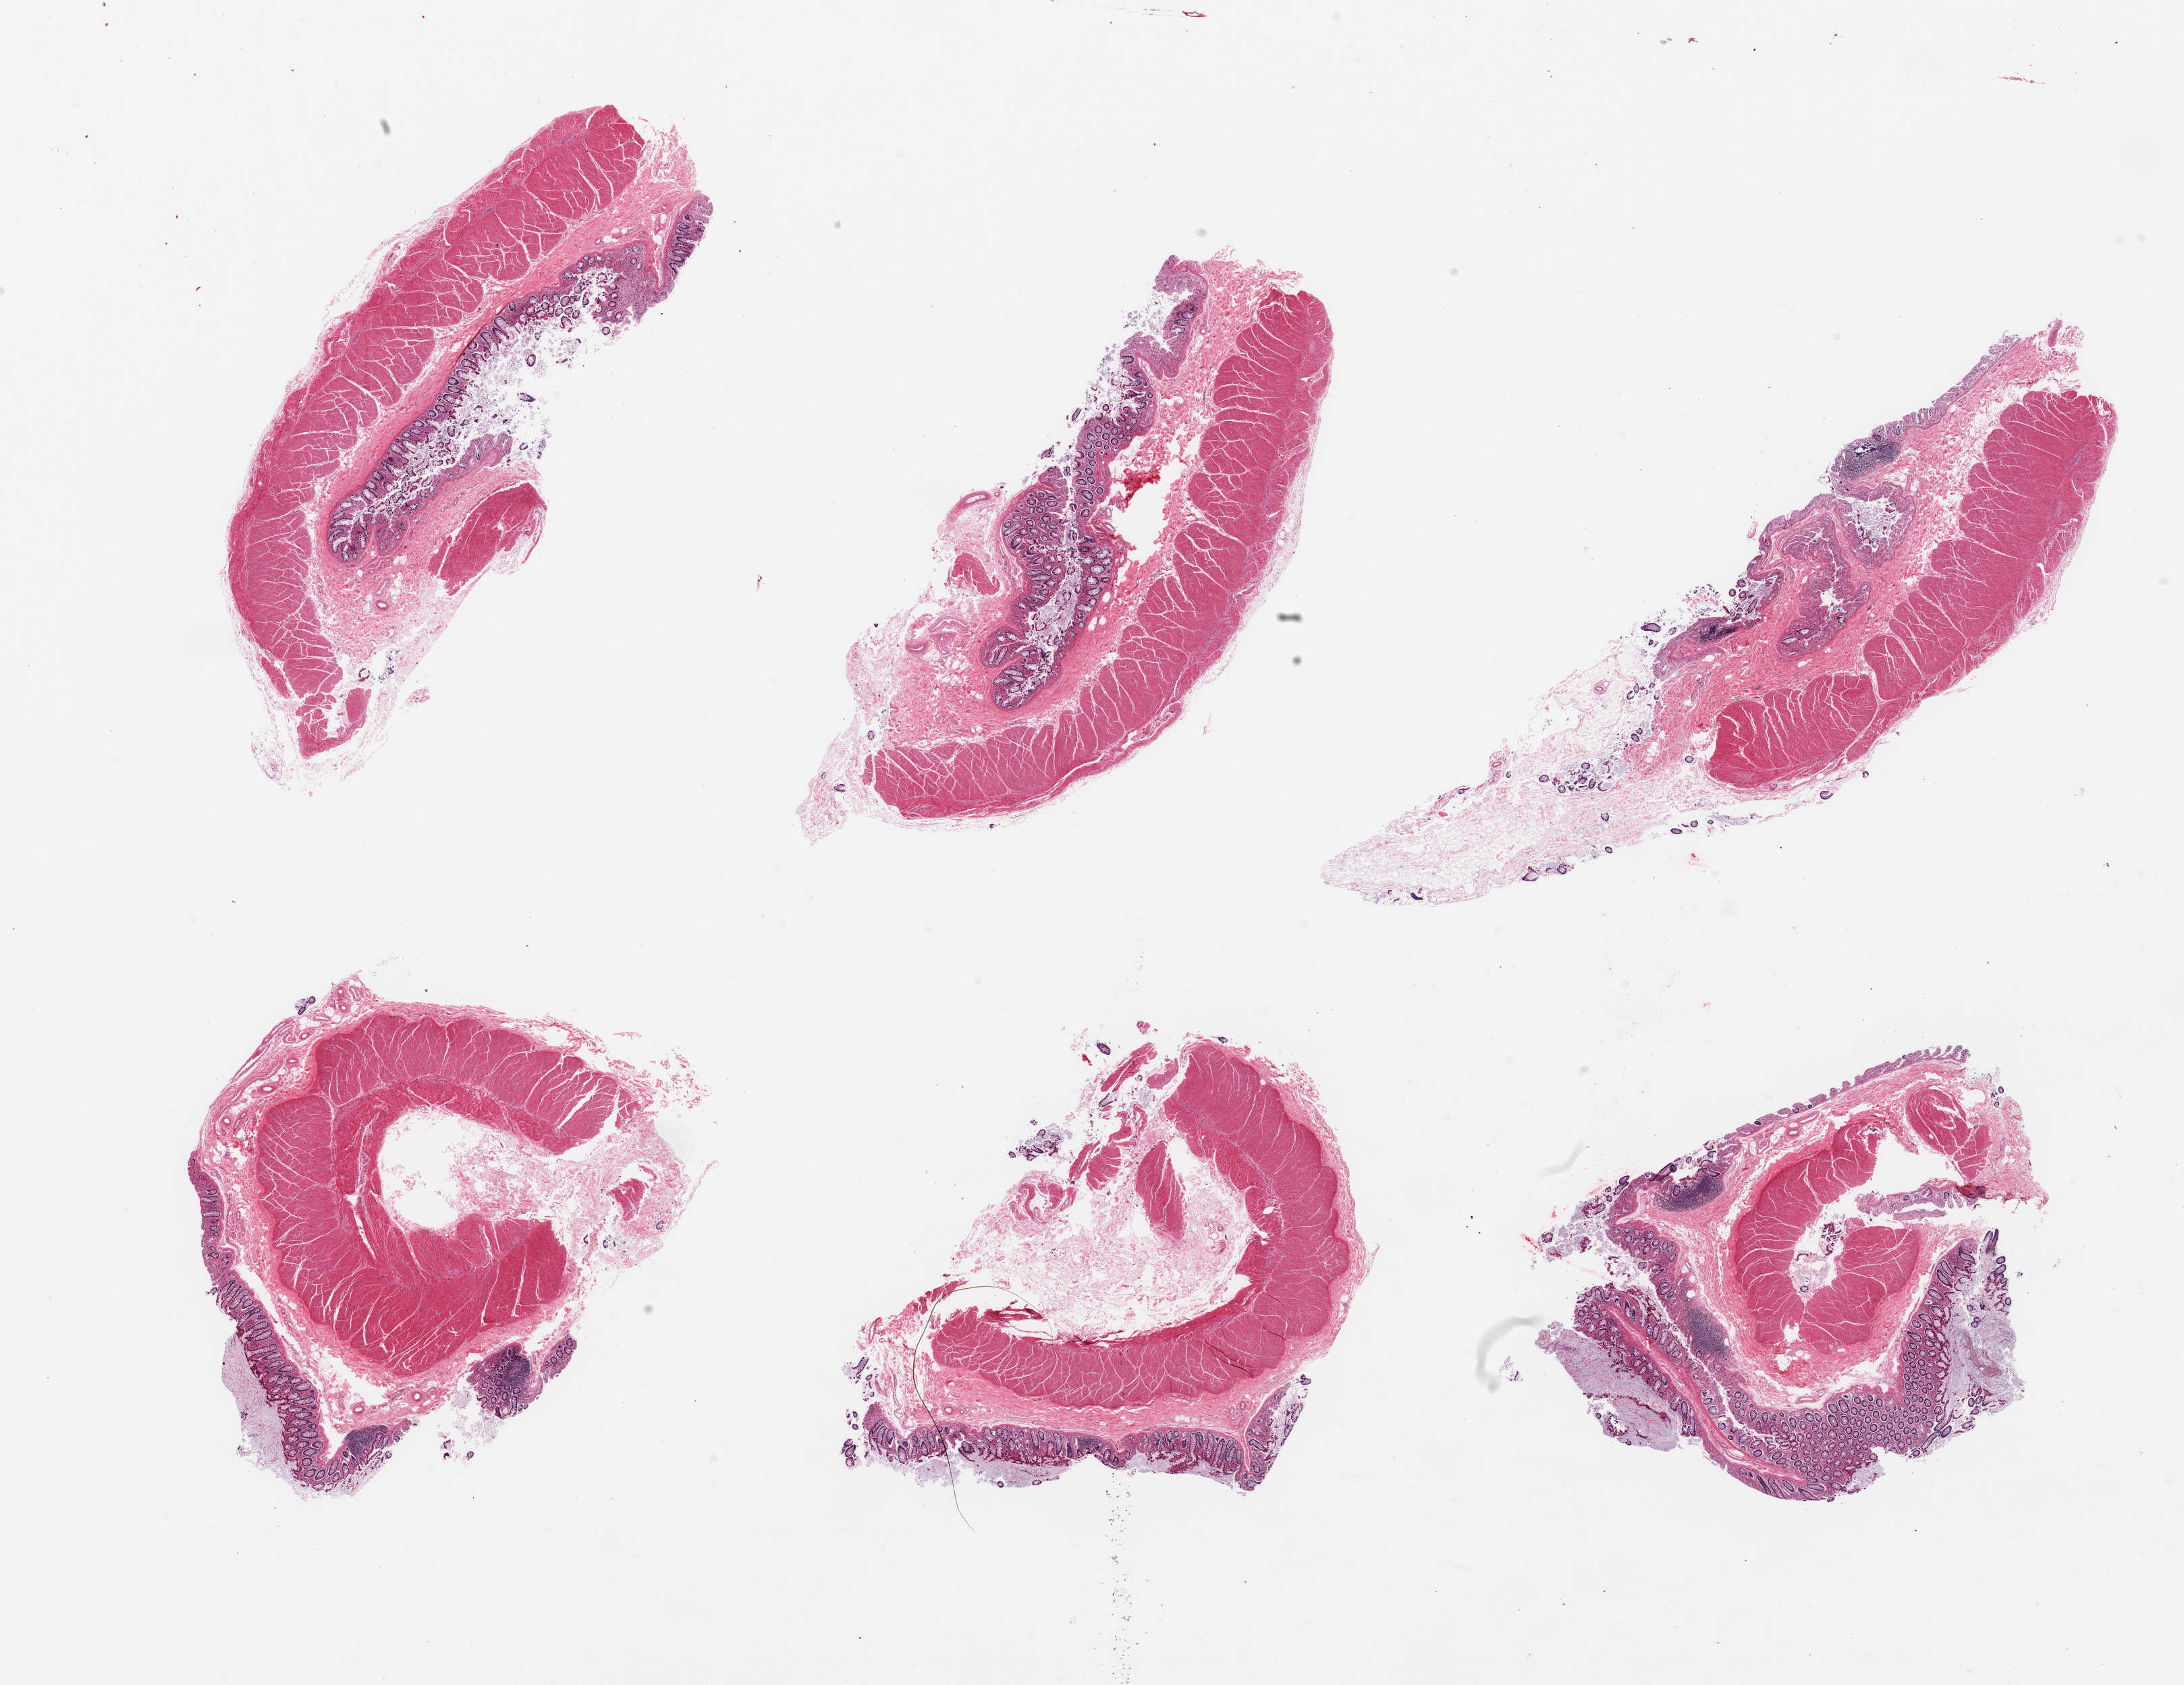
Haematoxylin and eosin whole-slide image, brightfield, shown as a low-resolution overview of the whole scanned area (about 25.6 x 19.7 mm, from a 20x scan). PAXgene-fixed, paraffin-embedded tissue. Target tissue: sigmoid colon. Tissue donor sample.
Reviewer comment on this tissue sample: 6 pieces; full thickness colon.